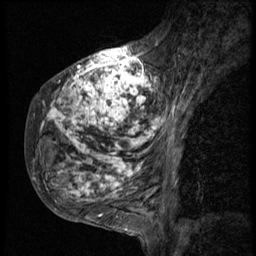
Breast MRI (dynamic contrast-enhanced), one sagittal slice; position 18 of 58 along the scan axis; 3 images stored at this slice position (order not interpretable as contrast timing); 1.5 T; TE 4.2 ms, TR 9 ms; 256 × 256 image matrix, field of view 180 × 180 mm. Female patient, age 50 years. From the clinical record (not read from this slice): setting: breast cancer imaged before/during neoadjuvant chemotherapy; receptor status: triple-negative.
Structures marked on this image (semi-automatic segmentation, software-assisted and operator-edited):
- analysis volume of interest (the breast-tissue region the enhancement analysis was run in; not a lesion): bounding box (x1, y1, x2, y2) in pixels: (26, 48, 186, 214)
- tumour enhancement mask (voxels above the 140 % enhancement threshold inside the analysis volume of interest): (33, 48, 186, 201)